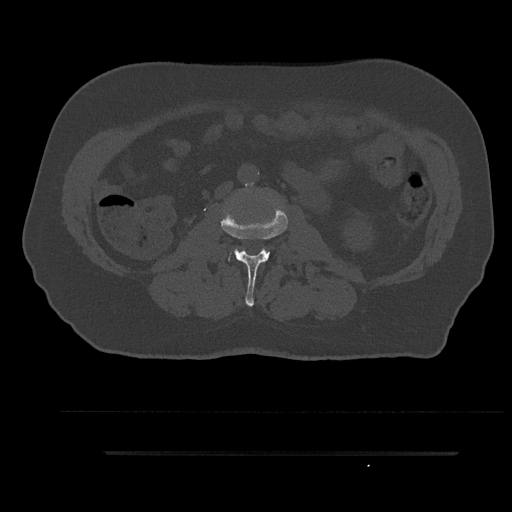
CT including the spine, one axial slice; position 90 of 797 along the scan axis; reconstruction kernel Br40s/3; 120 kVp; bone window (W 1800 / L 400 HU); 0.5 mm slice thickness; 512 × 512 image matrix. Male patient, age 63 years. From the clinical record (not read from this slice): primary cancer: renal; vertebrae with lytic lesions (as recorded): T8.
Structures marked on this image (semi-automatically segmented with operator editing):
- L2 vertebra: bounding box <221,207,288,307> (left, top, right, bottom; pixels)